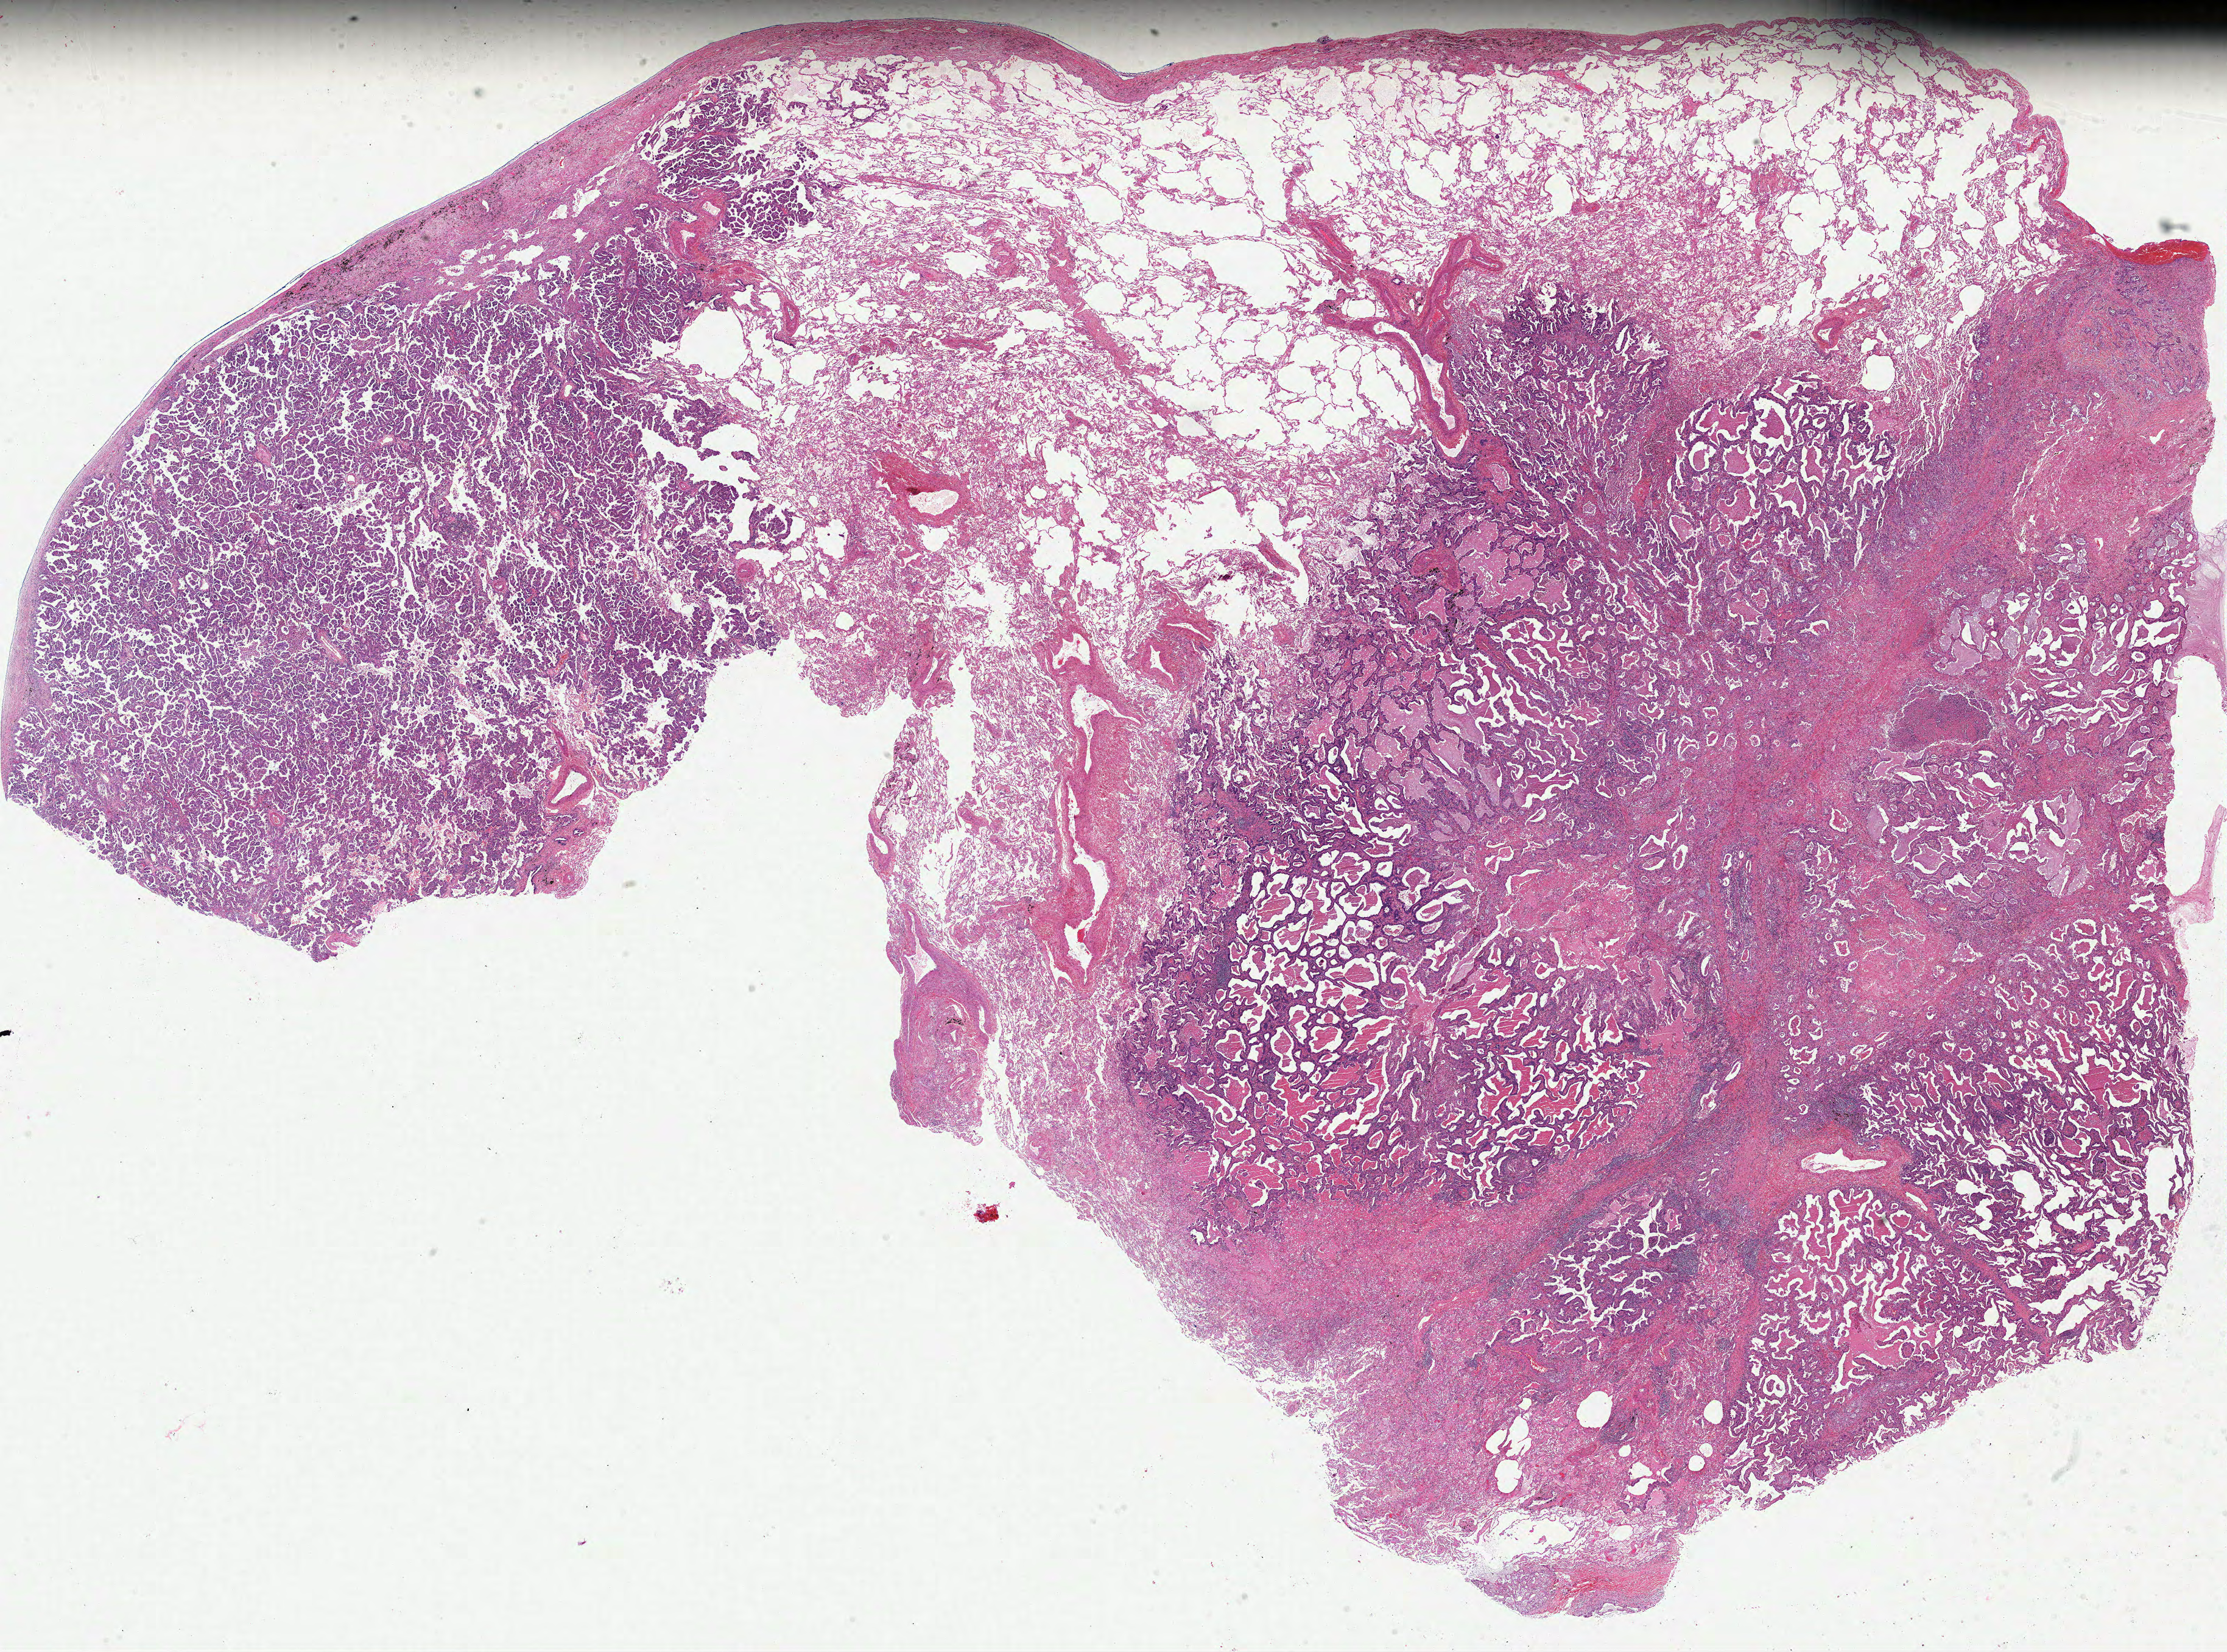
Whole-slide histology image, Hematoxylin and eosin (H&E) stained, shown as a low-resolution overview of the whole scanned area (about 29.5 x 21.9 mm, slide scanned at 40x). Formalin-fixed paraffin-embedded (FFPE) diagnostic section. Lung, primary tumour sample. Male, age 67 years at initial diagnosis.
AJCC pathologic stage: IB (6th edition). Diagnosis: Adenocarcinoma with mixed subtypes (upper lobe, lung).